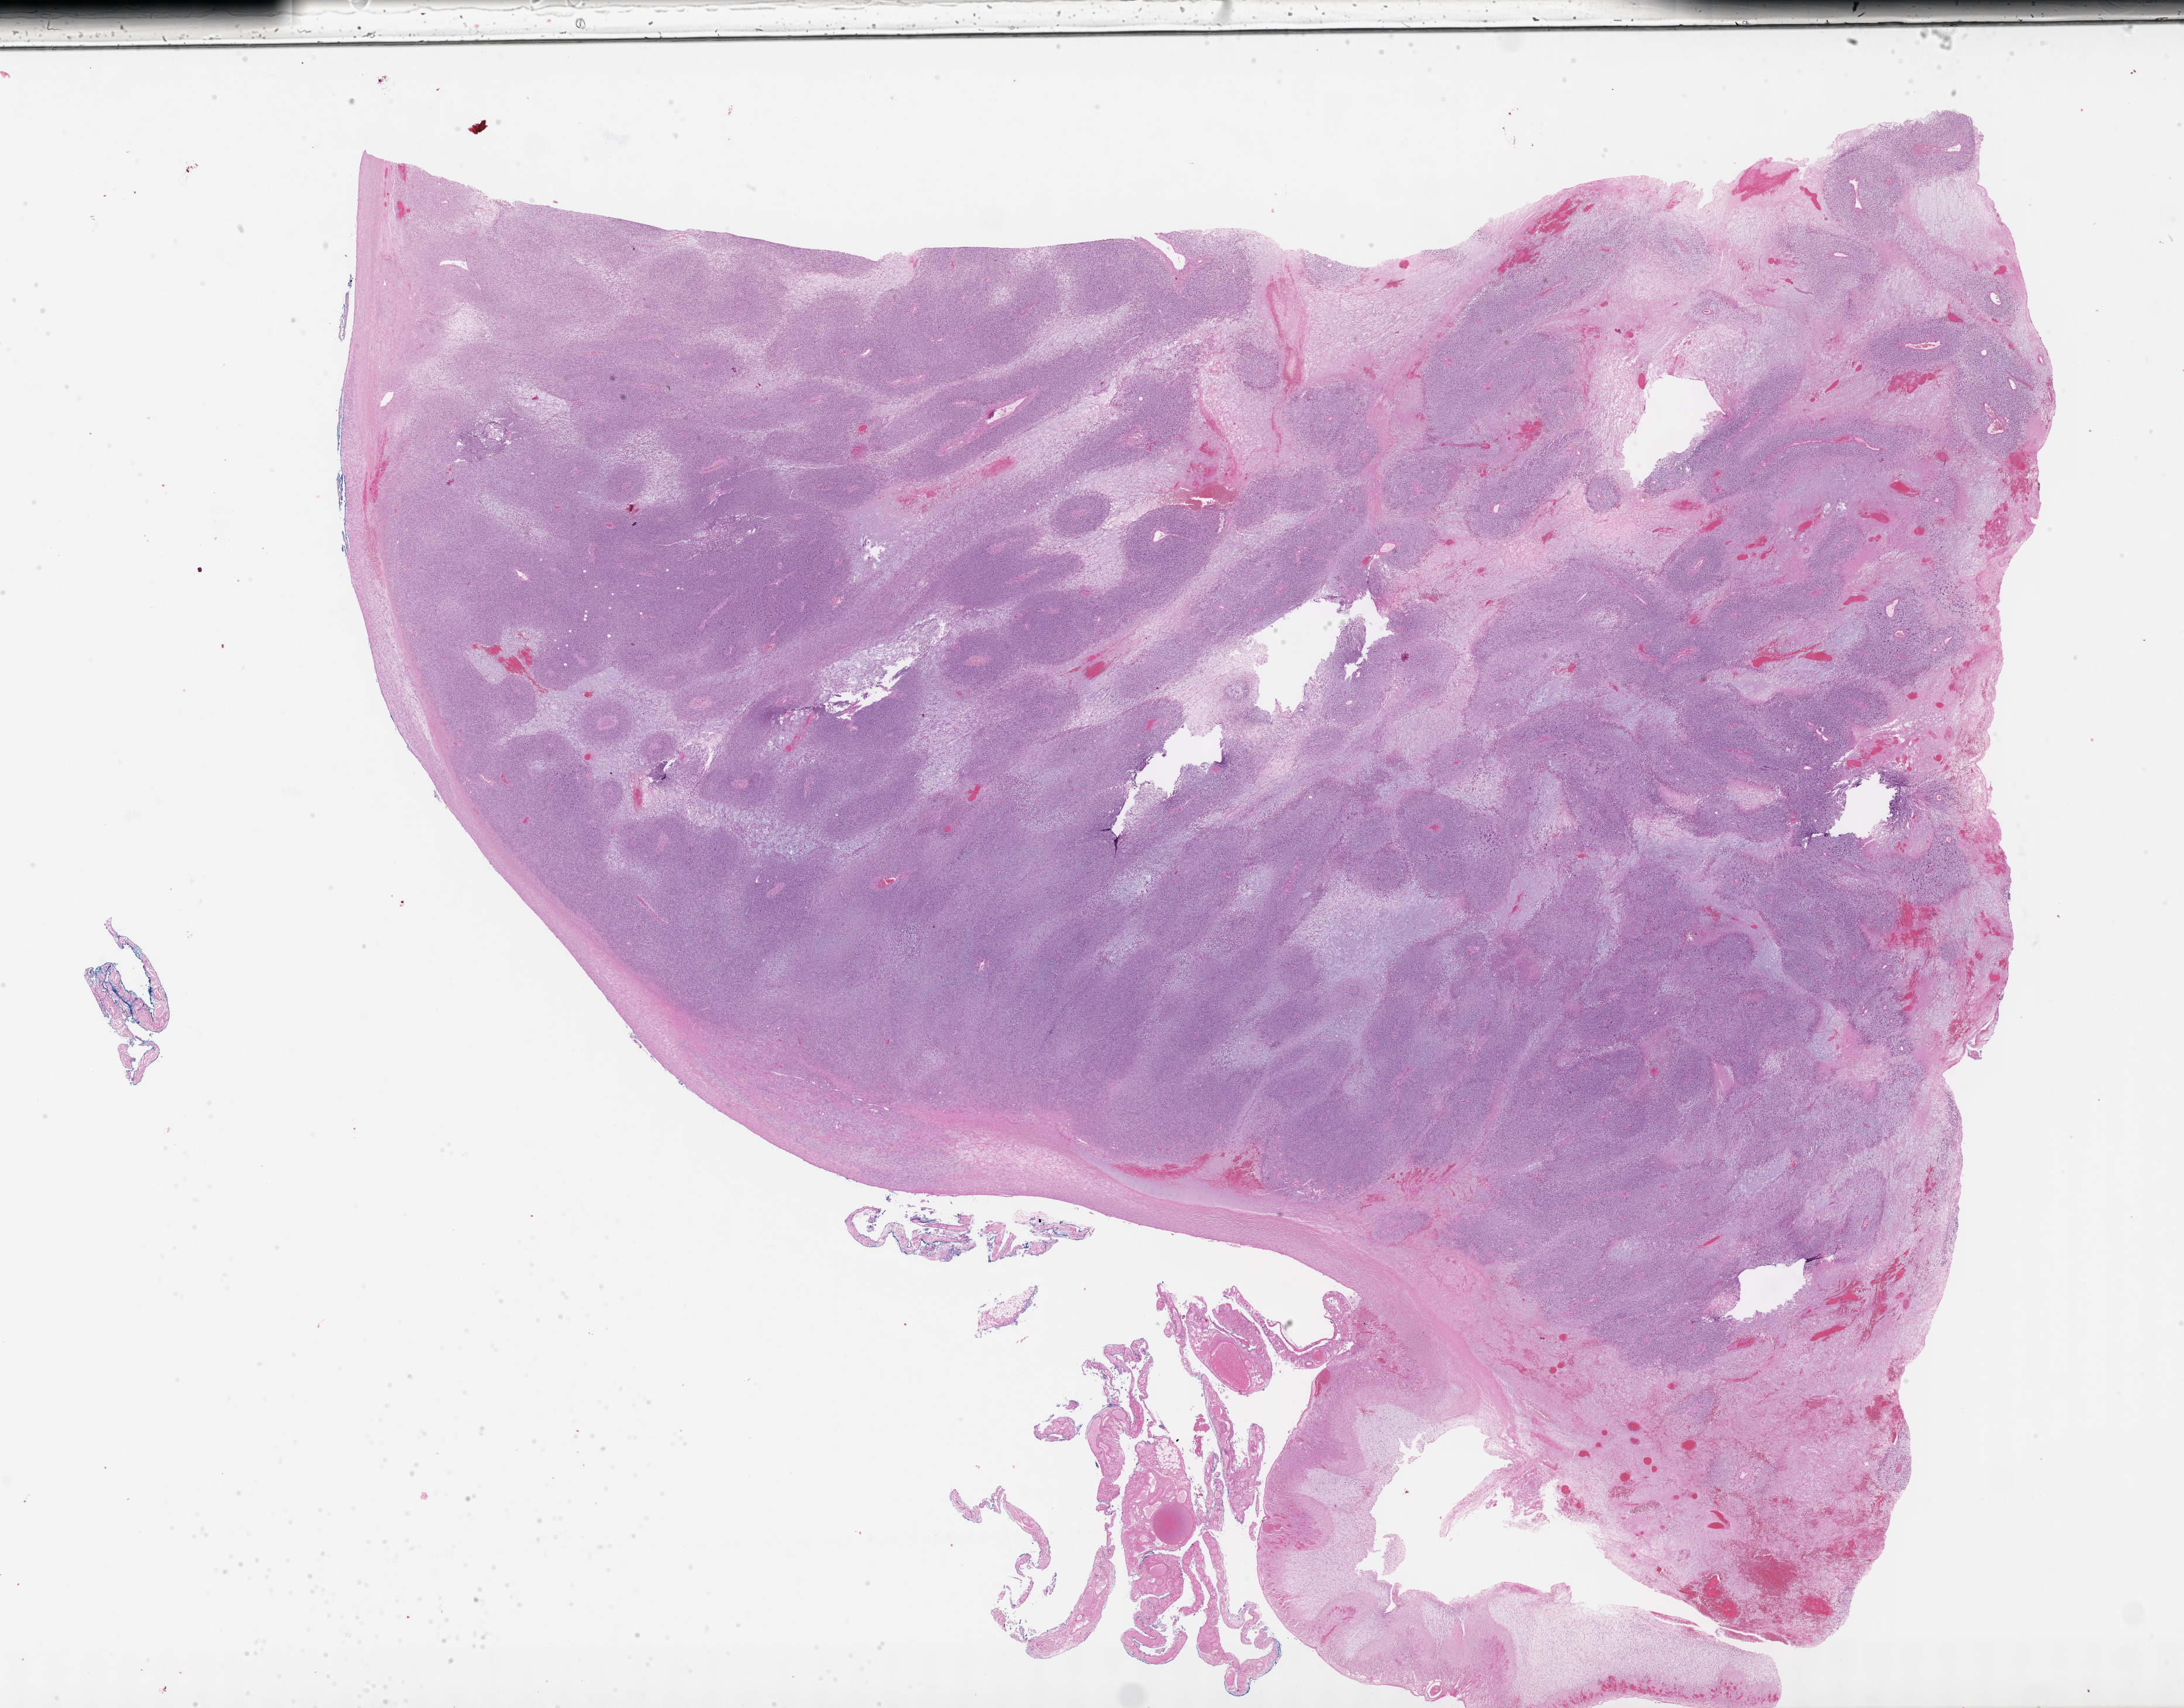
Digitized haematoxylin and eosin-stained section of tumor tissue — whole scanned area (about 30.2 x 23.6 mm) shown as a low-resolution overview, FFPE section, sample anatomic site: tonsil-right. Patient: female, age 3.7 years at diagnosis.
* diagnosis: rhabdomyosarcoma; histological classification: embryonal rhabdomyosarcoma
* primary site (case record): retroperitoneum
* stage (as recorded): 4
* metastatic status at presentation (as recorded): metastatic